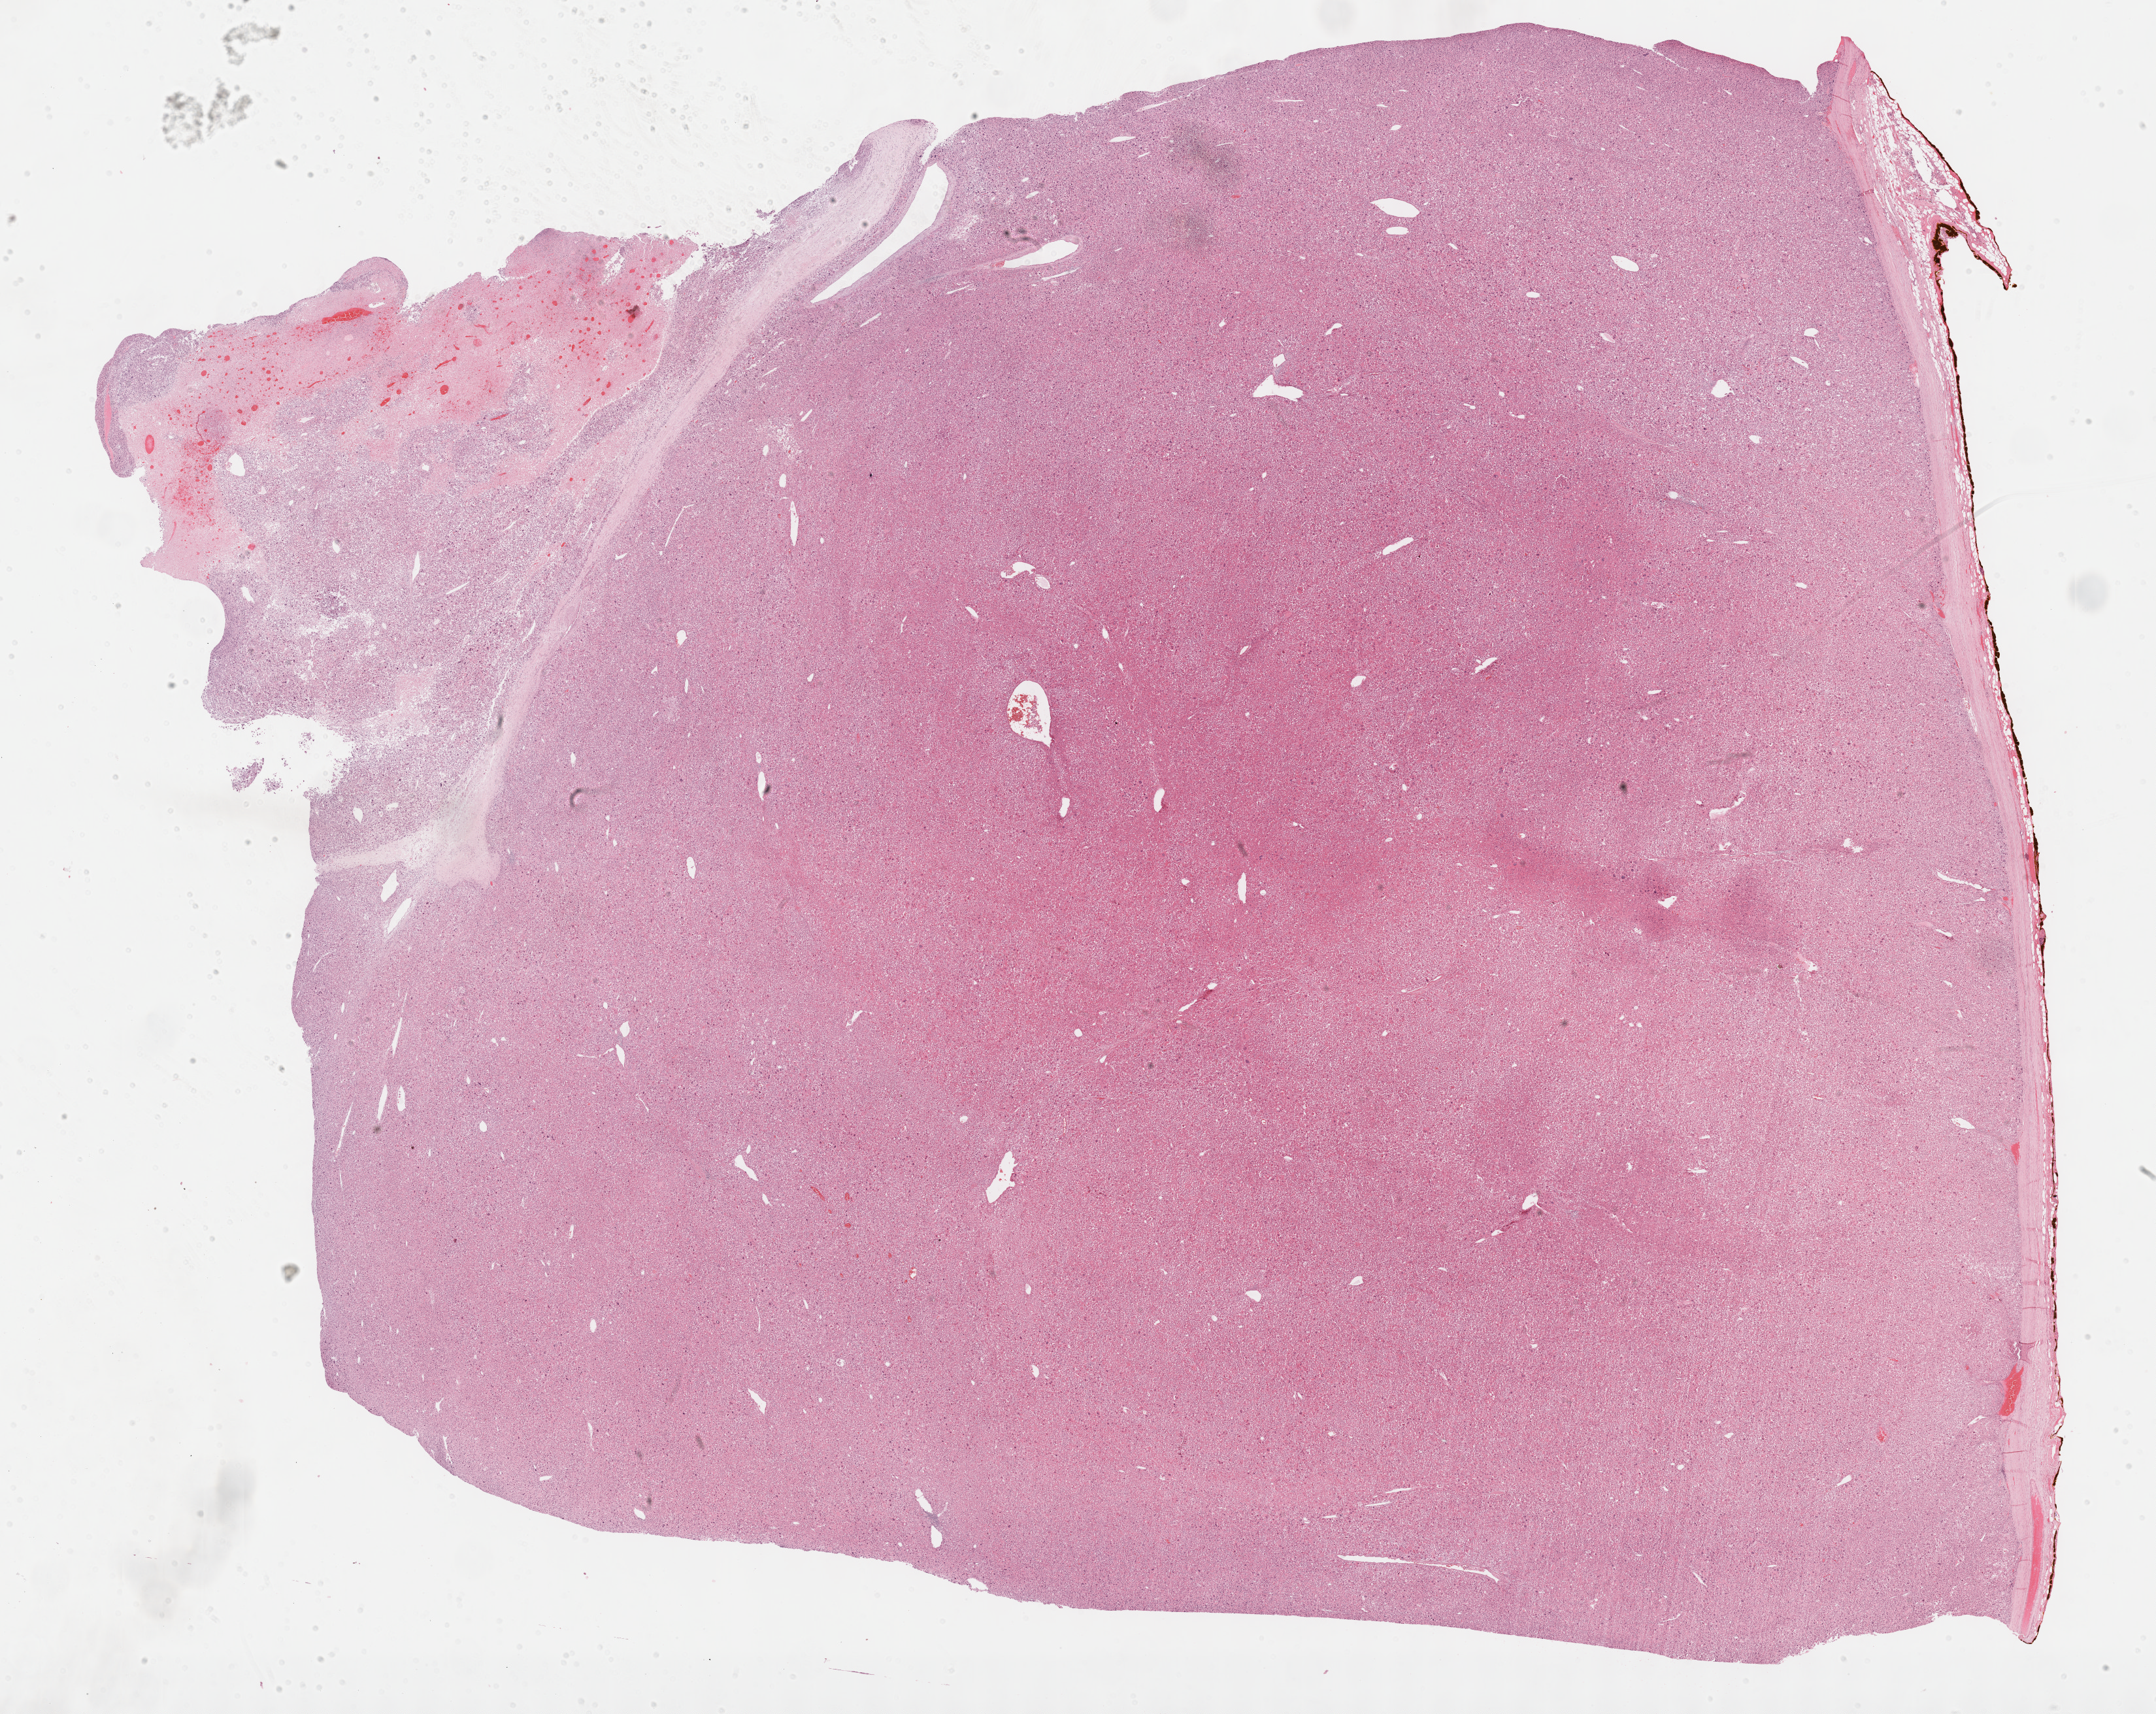
H&E-stained whole-slide image — a low-resolution overview of the entire scanned area, about 26.7 x 21.2 mm (from a 40x scan), FFPE section, sample: primary tumour, adrenal cortex. Patient: female, age at initial diagnosis 64 years.
Diagnosis: Adrenal cortical carcinoma (cortex of adrenal gland).